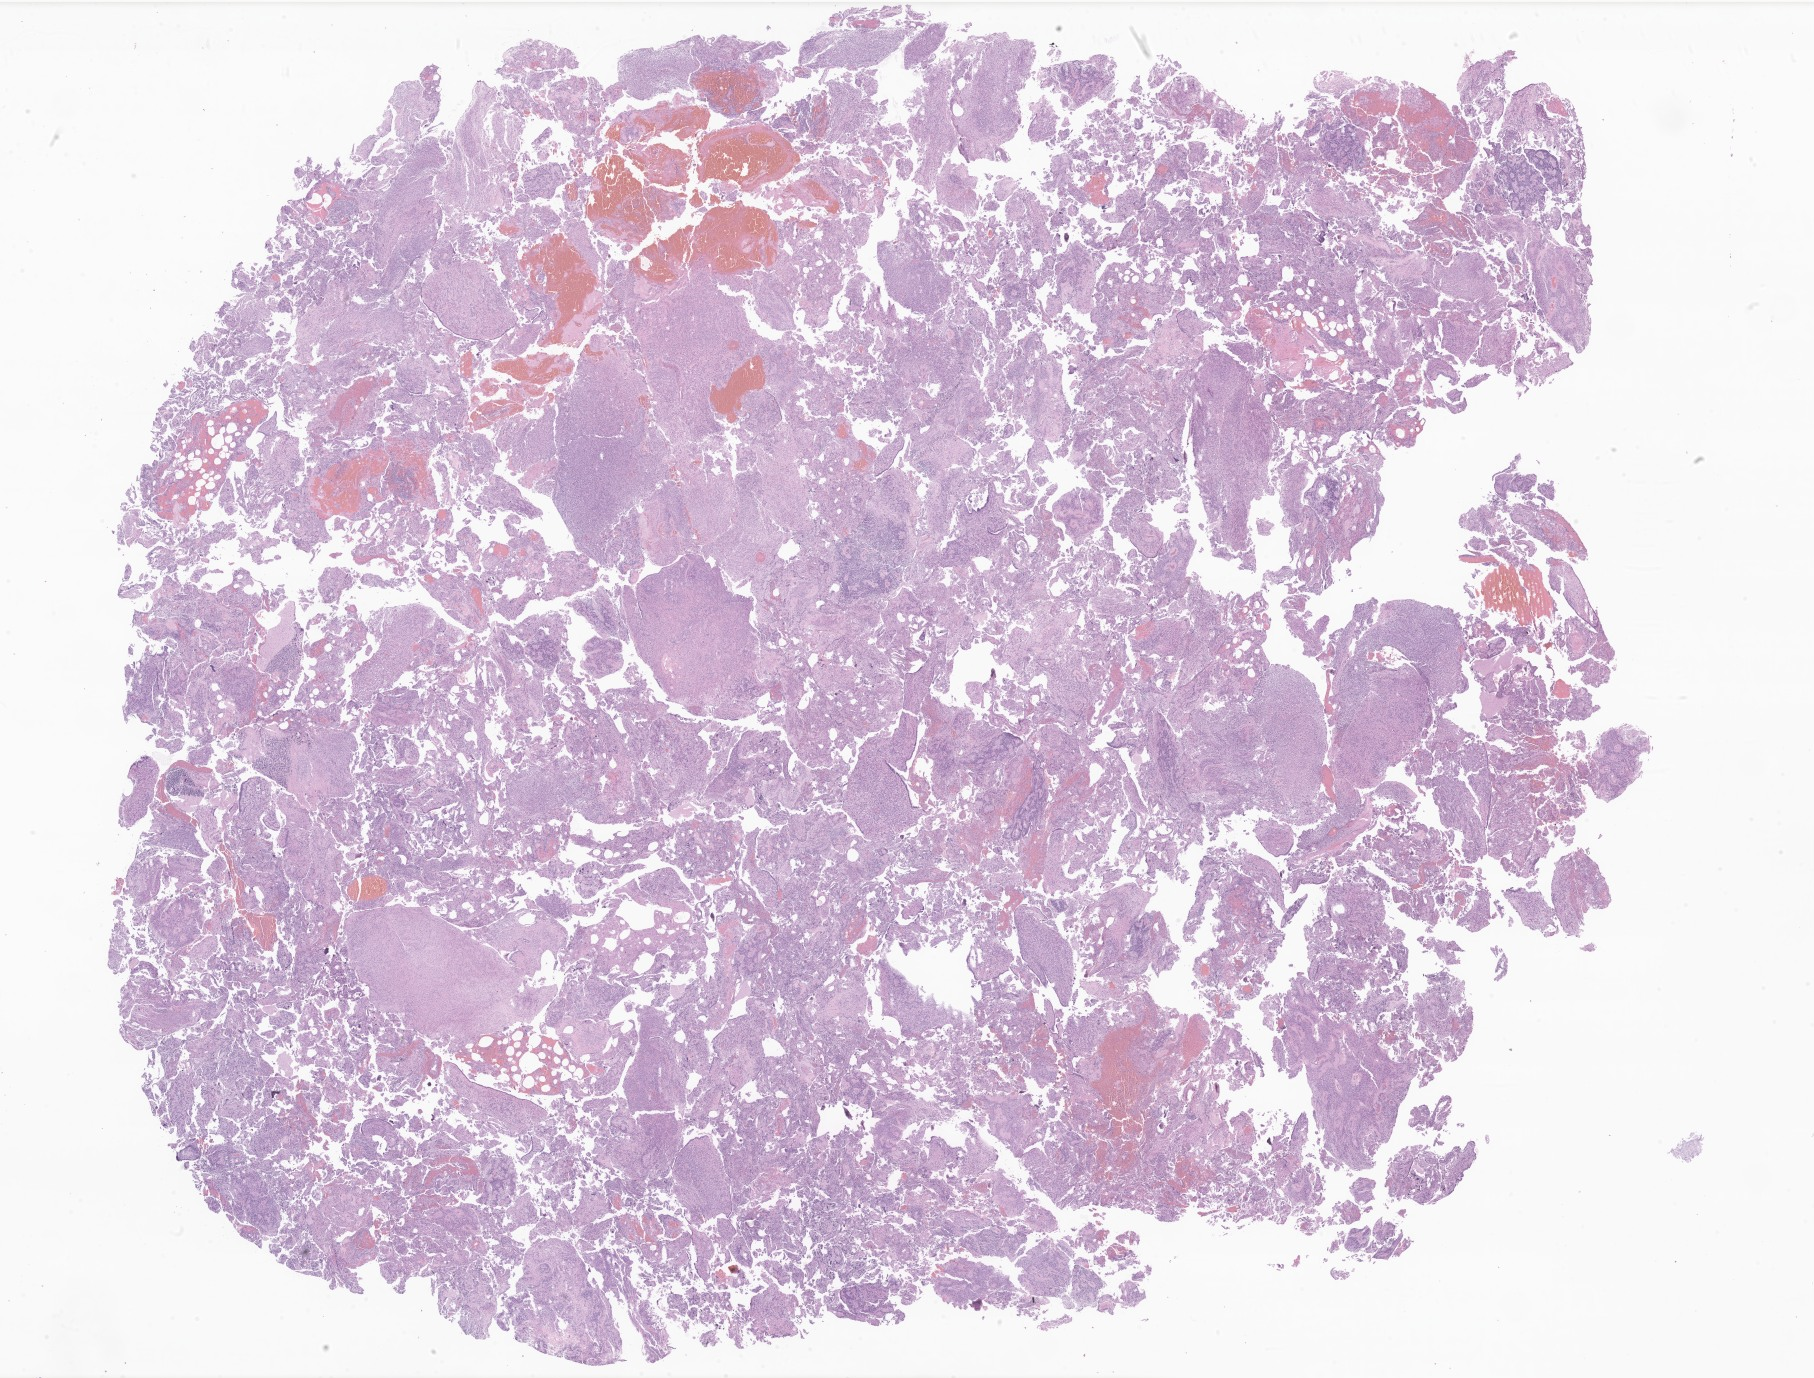
Haematoxylin and eosin whole-slide image of tumor tissue from the brain, a low-resolution overview of the entire scanned area, about 30.6 x 23.2 mm; formalin-fixed, paraffin-embedded (FFPE) tissue. Female patient, age 814 days (about 2.2 years).
Recorded diagnosis: Ependymoma, NOS.